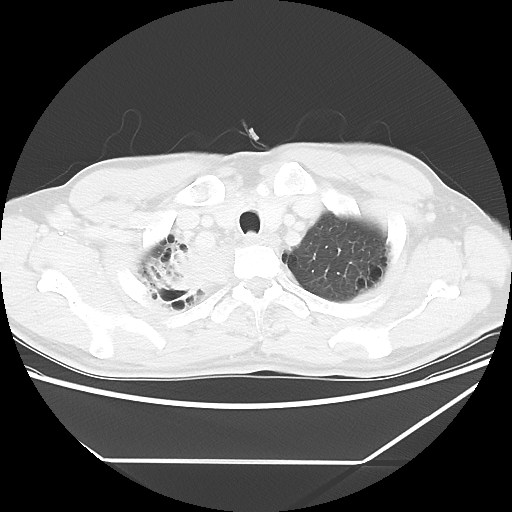
Chest CT, one axial slice; slice 54 of 60 in the series (ordered by position); reconstruction kernel LUNG; 120 kVp; lung window (W 1500 / L -600 HU); 5 mm slice thickness; 512 × 512 image matrix, field of view 367 × 367 mm. Male patient, age 58 years. Case-level facts recorded for this patient, not image findings: clinical TNM (as recorded): T2 N2 M0.
Outlined on this slice (rectangle marked by the reading radiologist):
- lung tumour (recorded histology: squamous cell carcinoma): box from (x=159, y=245) to (x=228, y=306) px